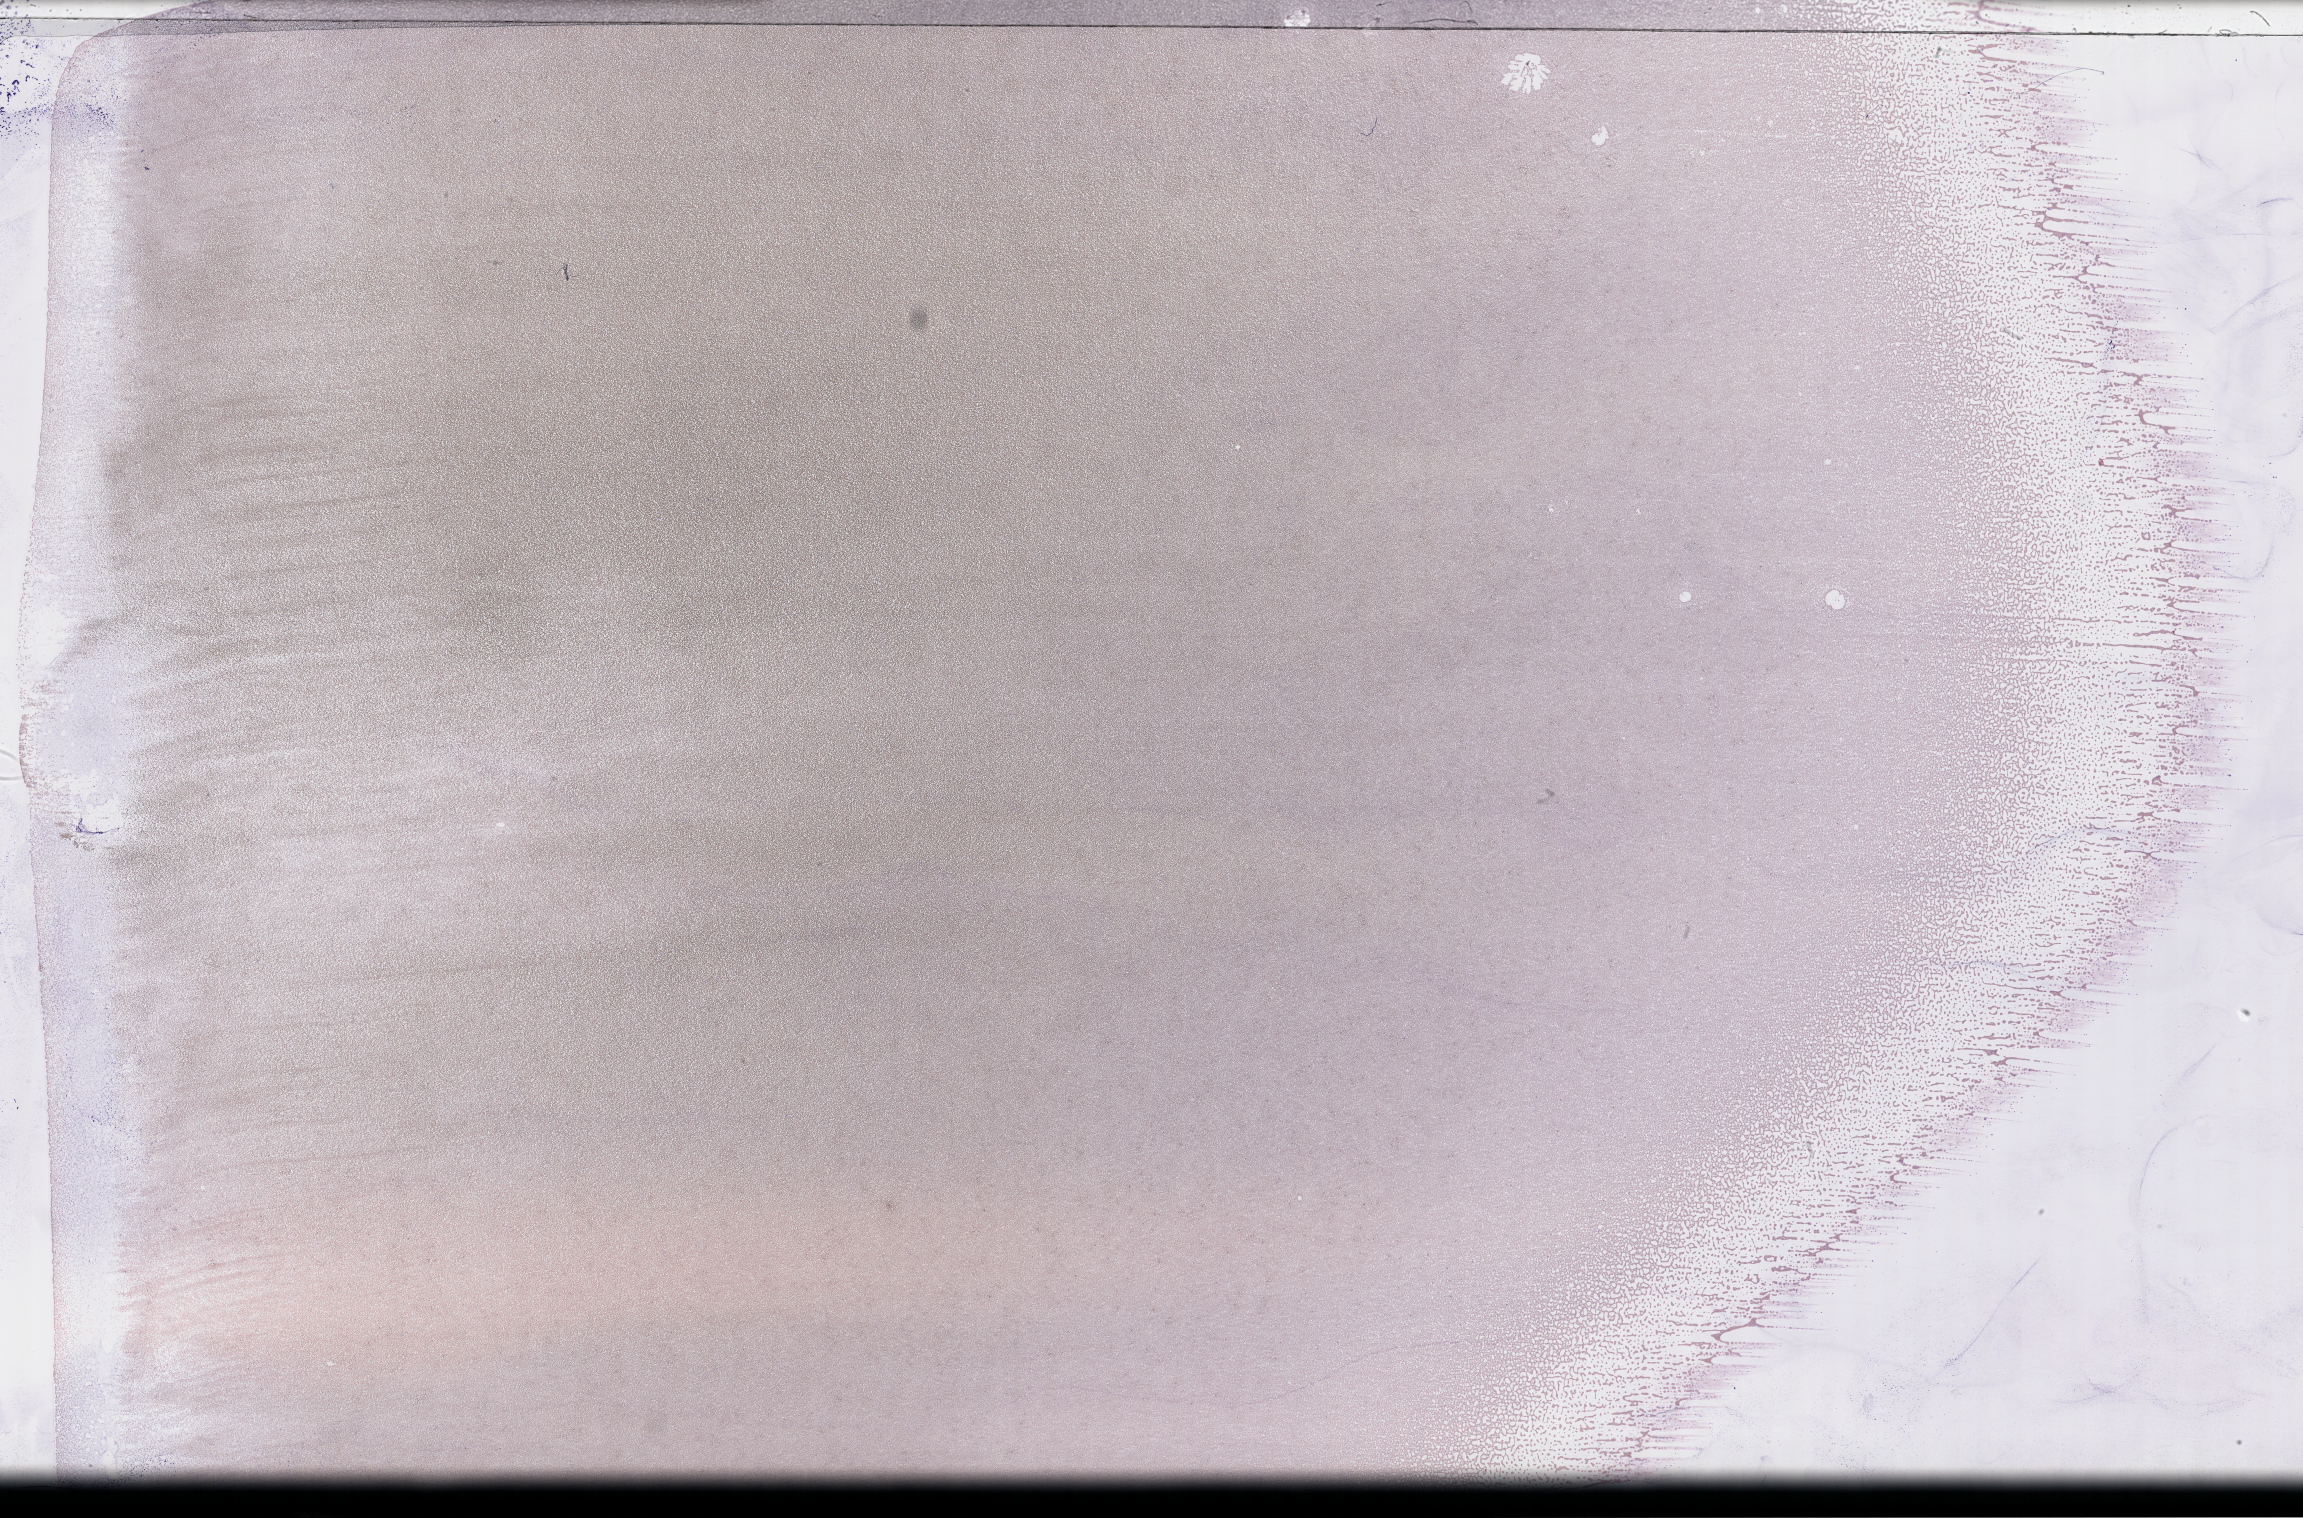
Wright–Giemsa-stained whole blood smear, whole-slide image — low-resolution overview of the scanned area, about 37.2 x 24.5 mm. Smear from an EDTA sample. Specimen time point: collected on treatment. Patient: male.
- from a patient with: Plasma Cell Myeloma